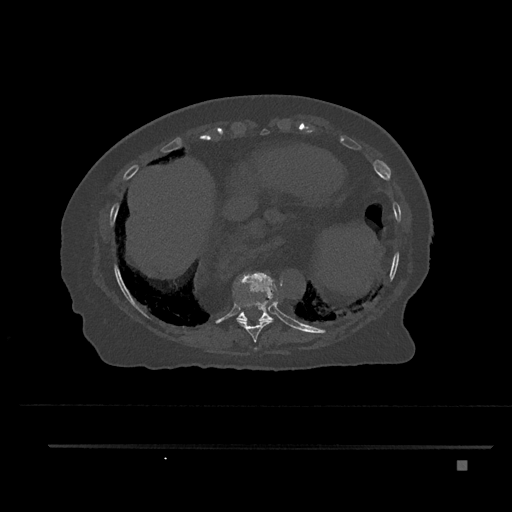
CT including the spine, one axial slice; position 380 of 797 along the scan axis; 120 kVp; bone window (W 1800 / L 400 HU); 0.5 mm slice thickness; 512 × 512 image matrix, field of view 437 × 437 mm. Female patient, age 76 years. Case-level facts recorded for this patient, not image findings: primary cancer: lung.
Outlined on this slice (semi-automatically segmented with operator editing):
- T10 vertebra: bounding box (x1, y1, x2, y2) in pixels: (237, 273, 274, 322)
- T8 vertebra: (255, 348, 257, 351)
- T9 vertebra: (234, 272, 271, 342)